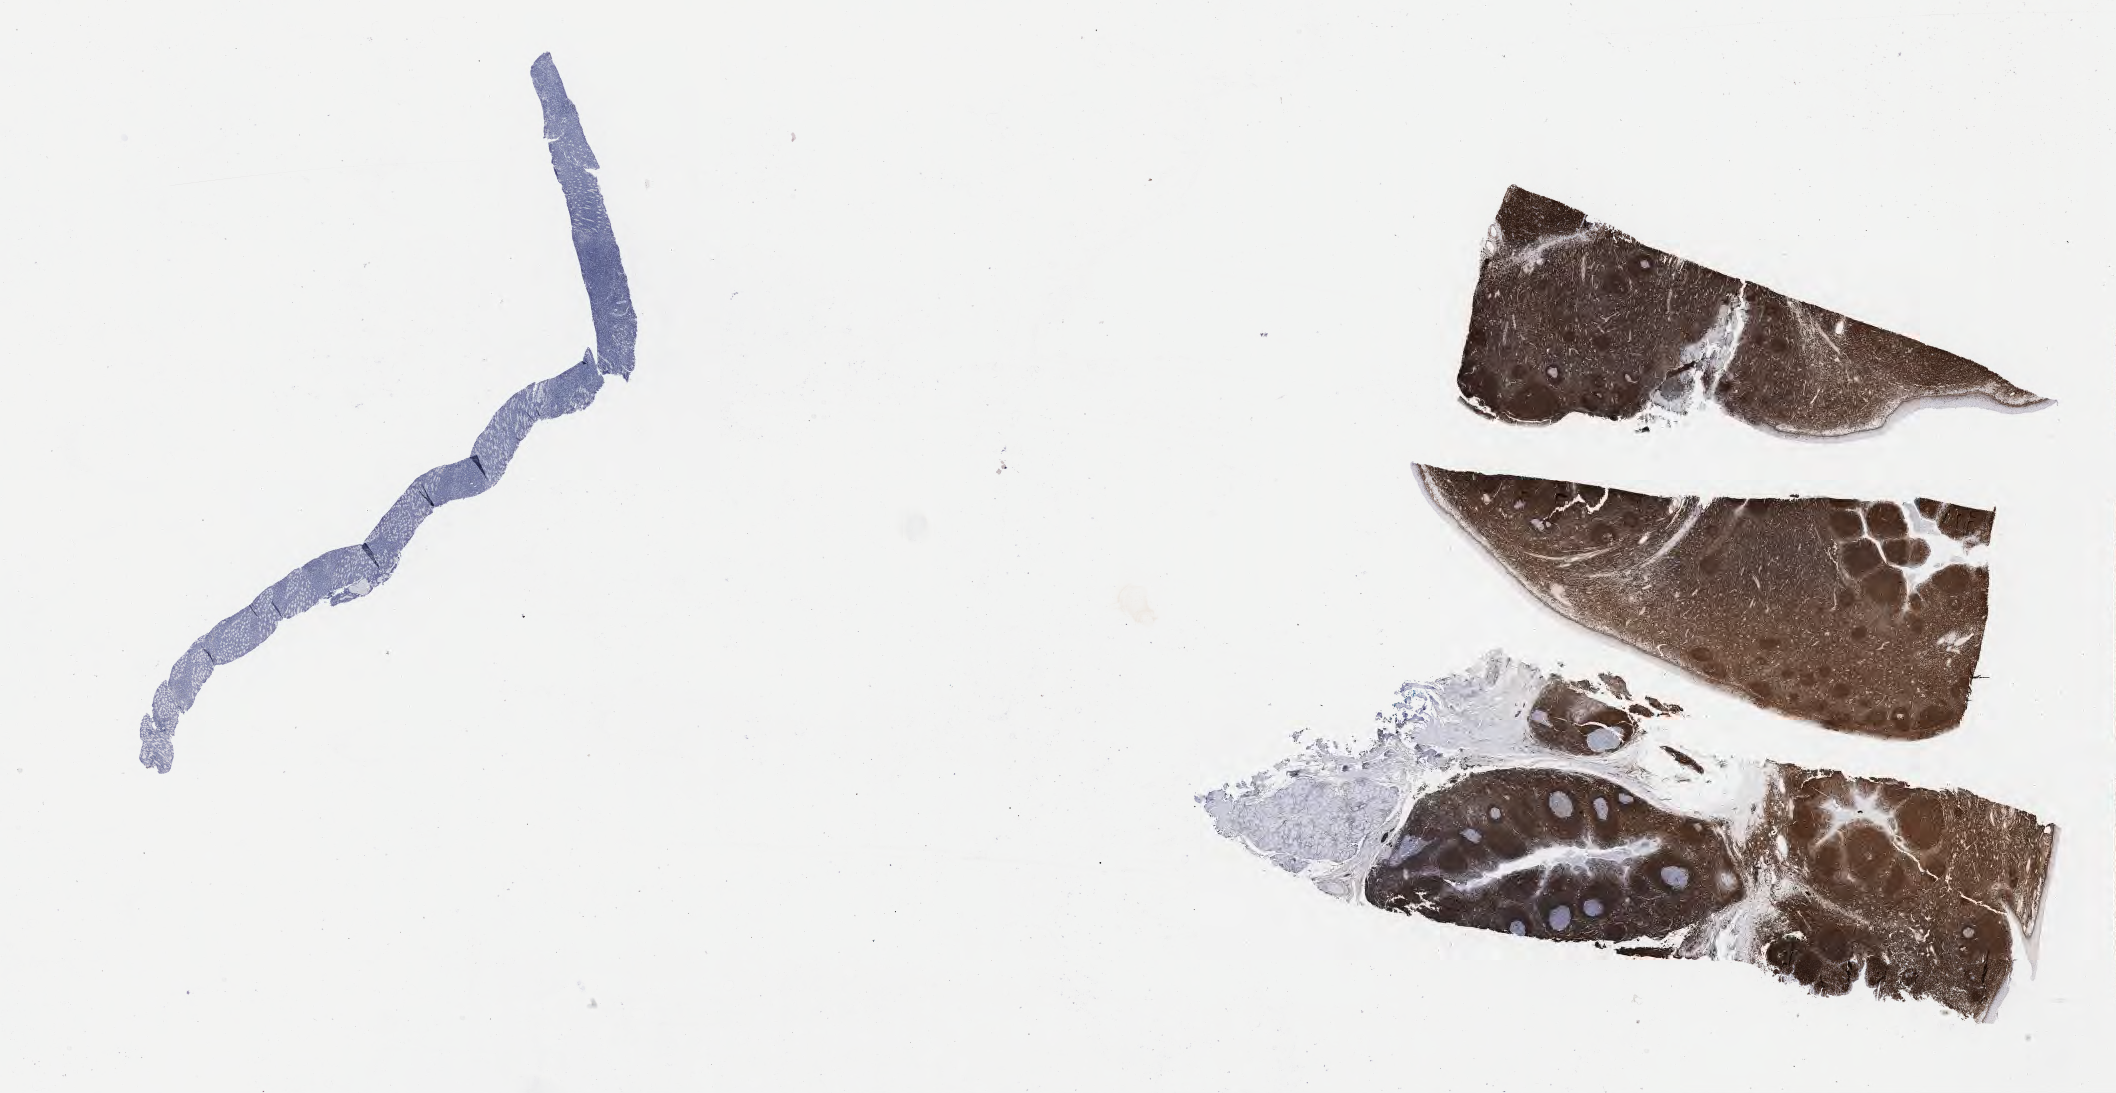
IHC for BCL2, whole-slide image, shown as a low-resolution overview of the whole scanned area (about 34.2 x 17.7 mm). Specimen: tumor tissue. Patient: male, age at initial diagnosis 4 years.
Diagnosis: Burkitt lymphoma, NOS.